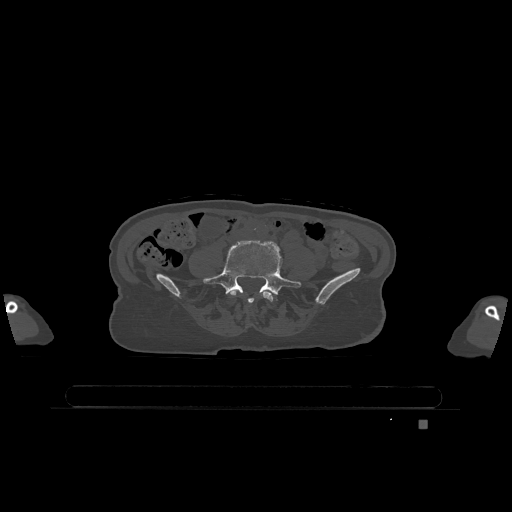
CT including the spine, one axial slice; slice 254 of 1317 in the series (ordered by position); bone window (W 1800 / L 400 HU); 0.5 mm slice thickness; 512 × 512 image matrix. Female patient, age 74 years. Case-level facts recorded for this patient, not image findings: primary cancer: lung; vertebrae with lytic lesions (as recorded): T1, T4, T5, T6, L4, L5.
Annotated regions visible in this slice (semi-automatic segmentation, software-assisted and operator-edited):
- L4 vertebra: bounding box (x1, y1, x2, y2) in pixels: (230, 290, 273, 302)
- L5 vertebra: (204, 240, 301, 303)